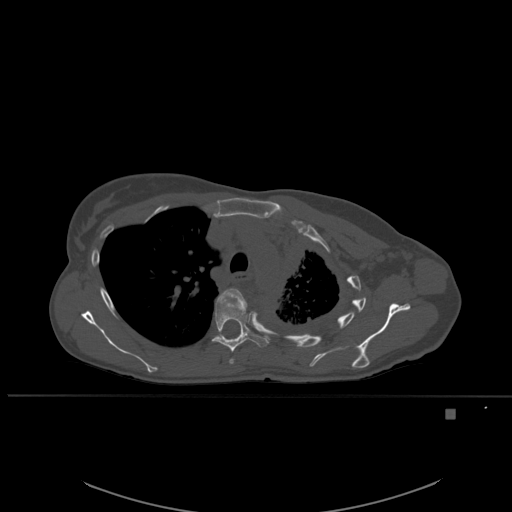
CT including the spine, one axial slice. Slice 401 of 537 in the series (ordered by position). Bone window (W 1800 / L 400 HU). 1.5 mm slice thickness. 512 × 512 image matrix. Female patient, age 45 years. Case-level facts recorded for this patient, not image findings: primary cancer: lung.
Outlined on this slice (semi-automatically segmented with operator editing):
- T4 vertebra: bounding box <221,288,247,364> (left, top, right, bottom; pixels)
- T5 vertebra: <212,295,269,353>